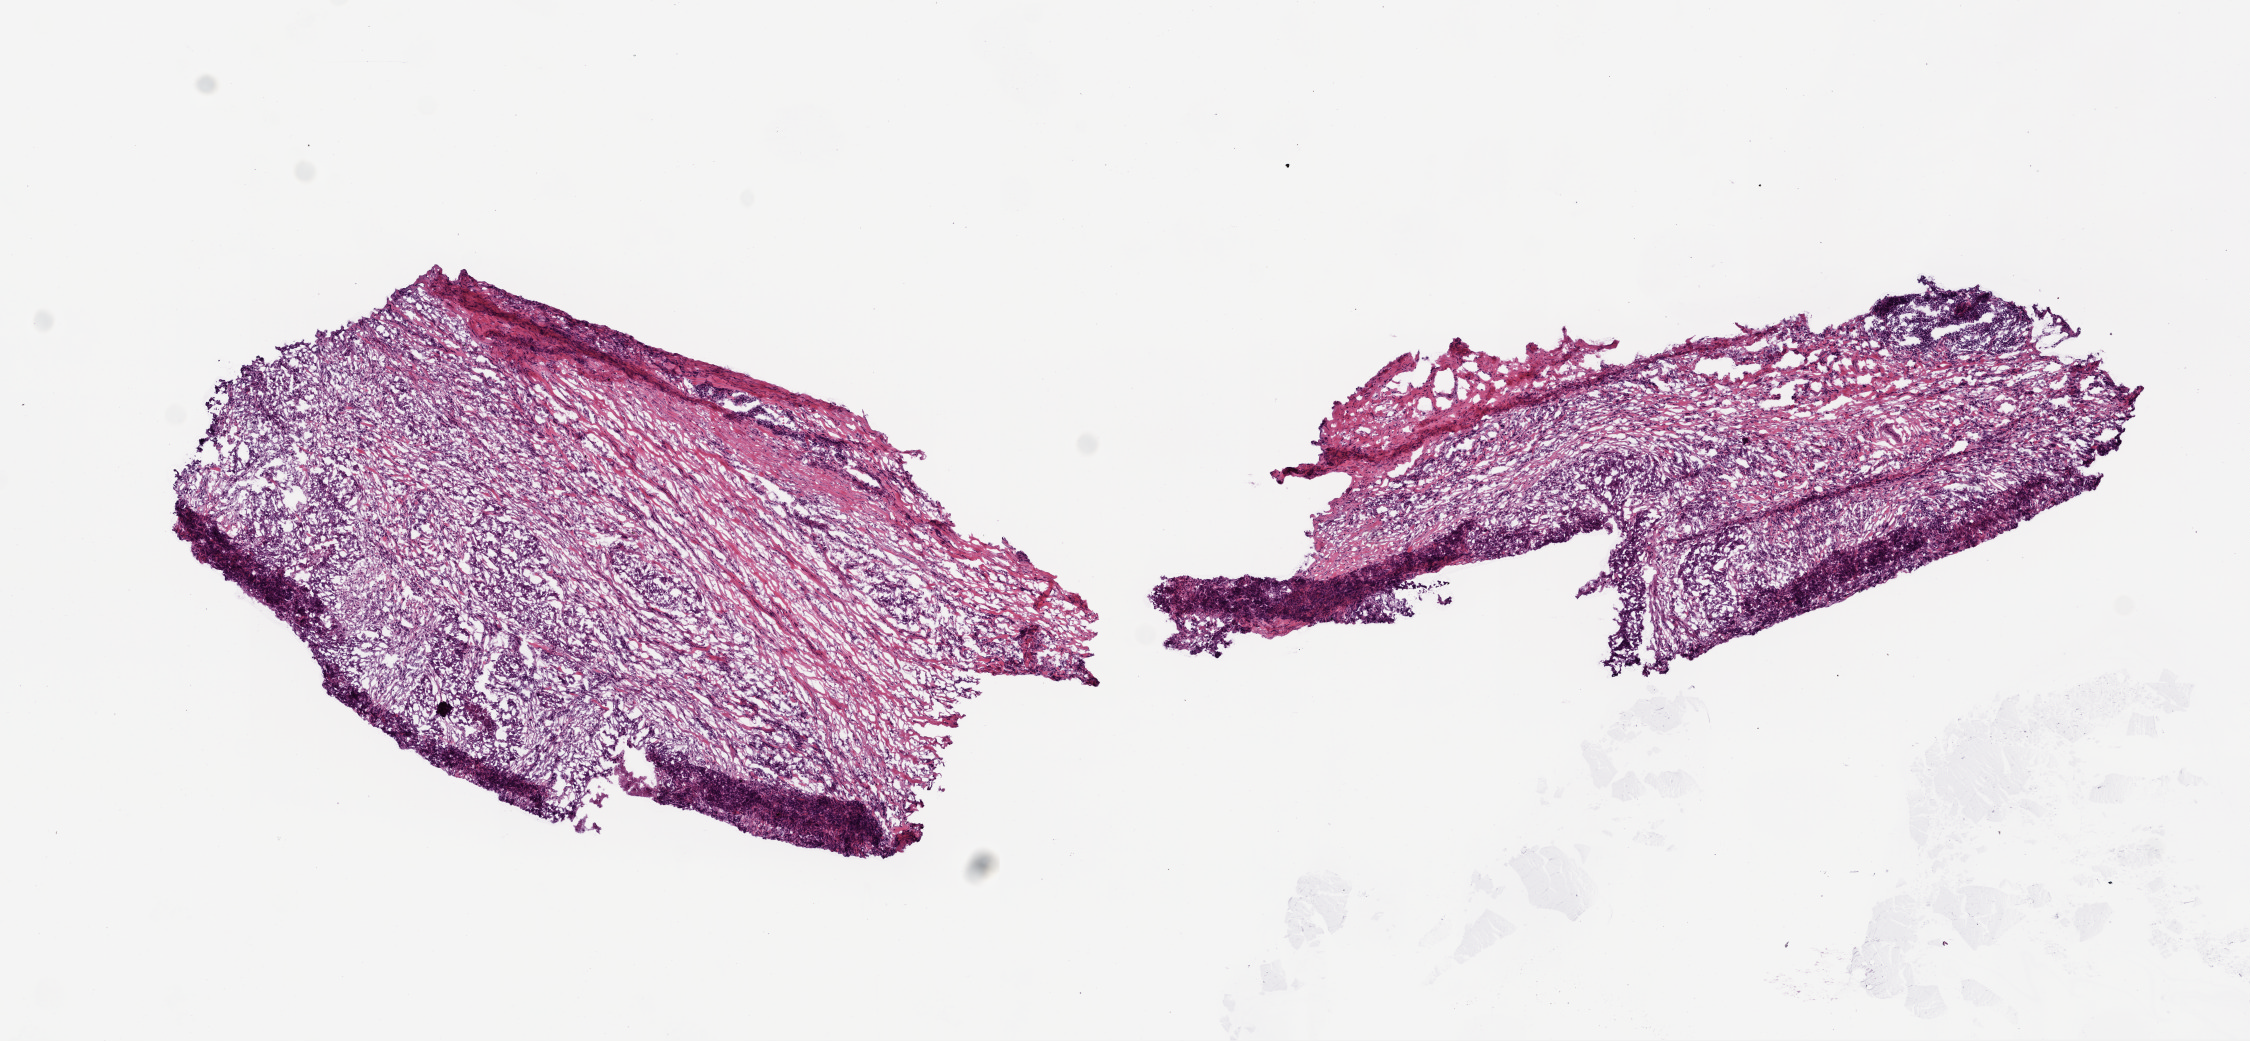
Digitized H&E tissue section (whole slide), shown as a low-resolution overview of the whole scanned area (about 9.0 x 4.2 mm, acquisition: 20x scan); frozen section from the top of the tissue portion; primary tumour sample from the head and neck. Male, age 73 years at initial diagnosis. Histologic grade: G3 (poorly differentiated). Slide review estimates, as recorded: tumour cells 40%, tumour nuclei 50%, normal cells 0%, stromal cells 60%, necrosis 0%.
- AJCC pathologic stage: IVA (7th edition)
- diagnosis: Squamous cell carcinoma, NOS (larynx, NOS)